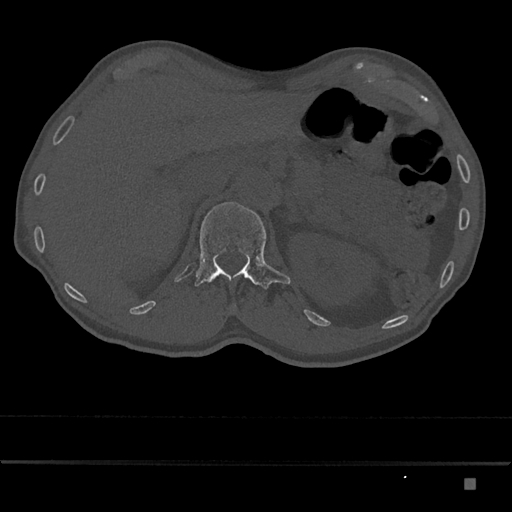
CT including the spine, one axial slice; position 554 of 797 along the scan axis; reconstruction kernel Br40s/3; 120 kVp; bone window (W 1800 / L 400 HU); 0.5 mm slice thickness; 512 × 512 image matrix, field of view 390 × 390 mm. Male patient, age 72 years. Case-level facts recorded for this patient, not image findings: primary cancer: prostate.
Outlined on this slice (semi-automatic segmentation, software-assisted and operator-edited):
- L1 vertebra: bounding box [x1, y1, x2, y2] px = [195, 202, 291, 289]
- T12 vertebra: [211, 279, 213, 281]